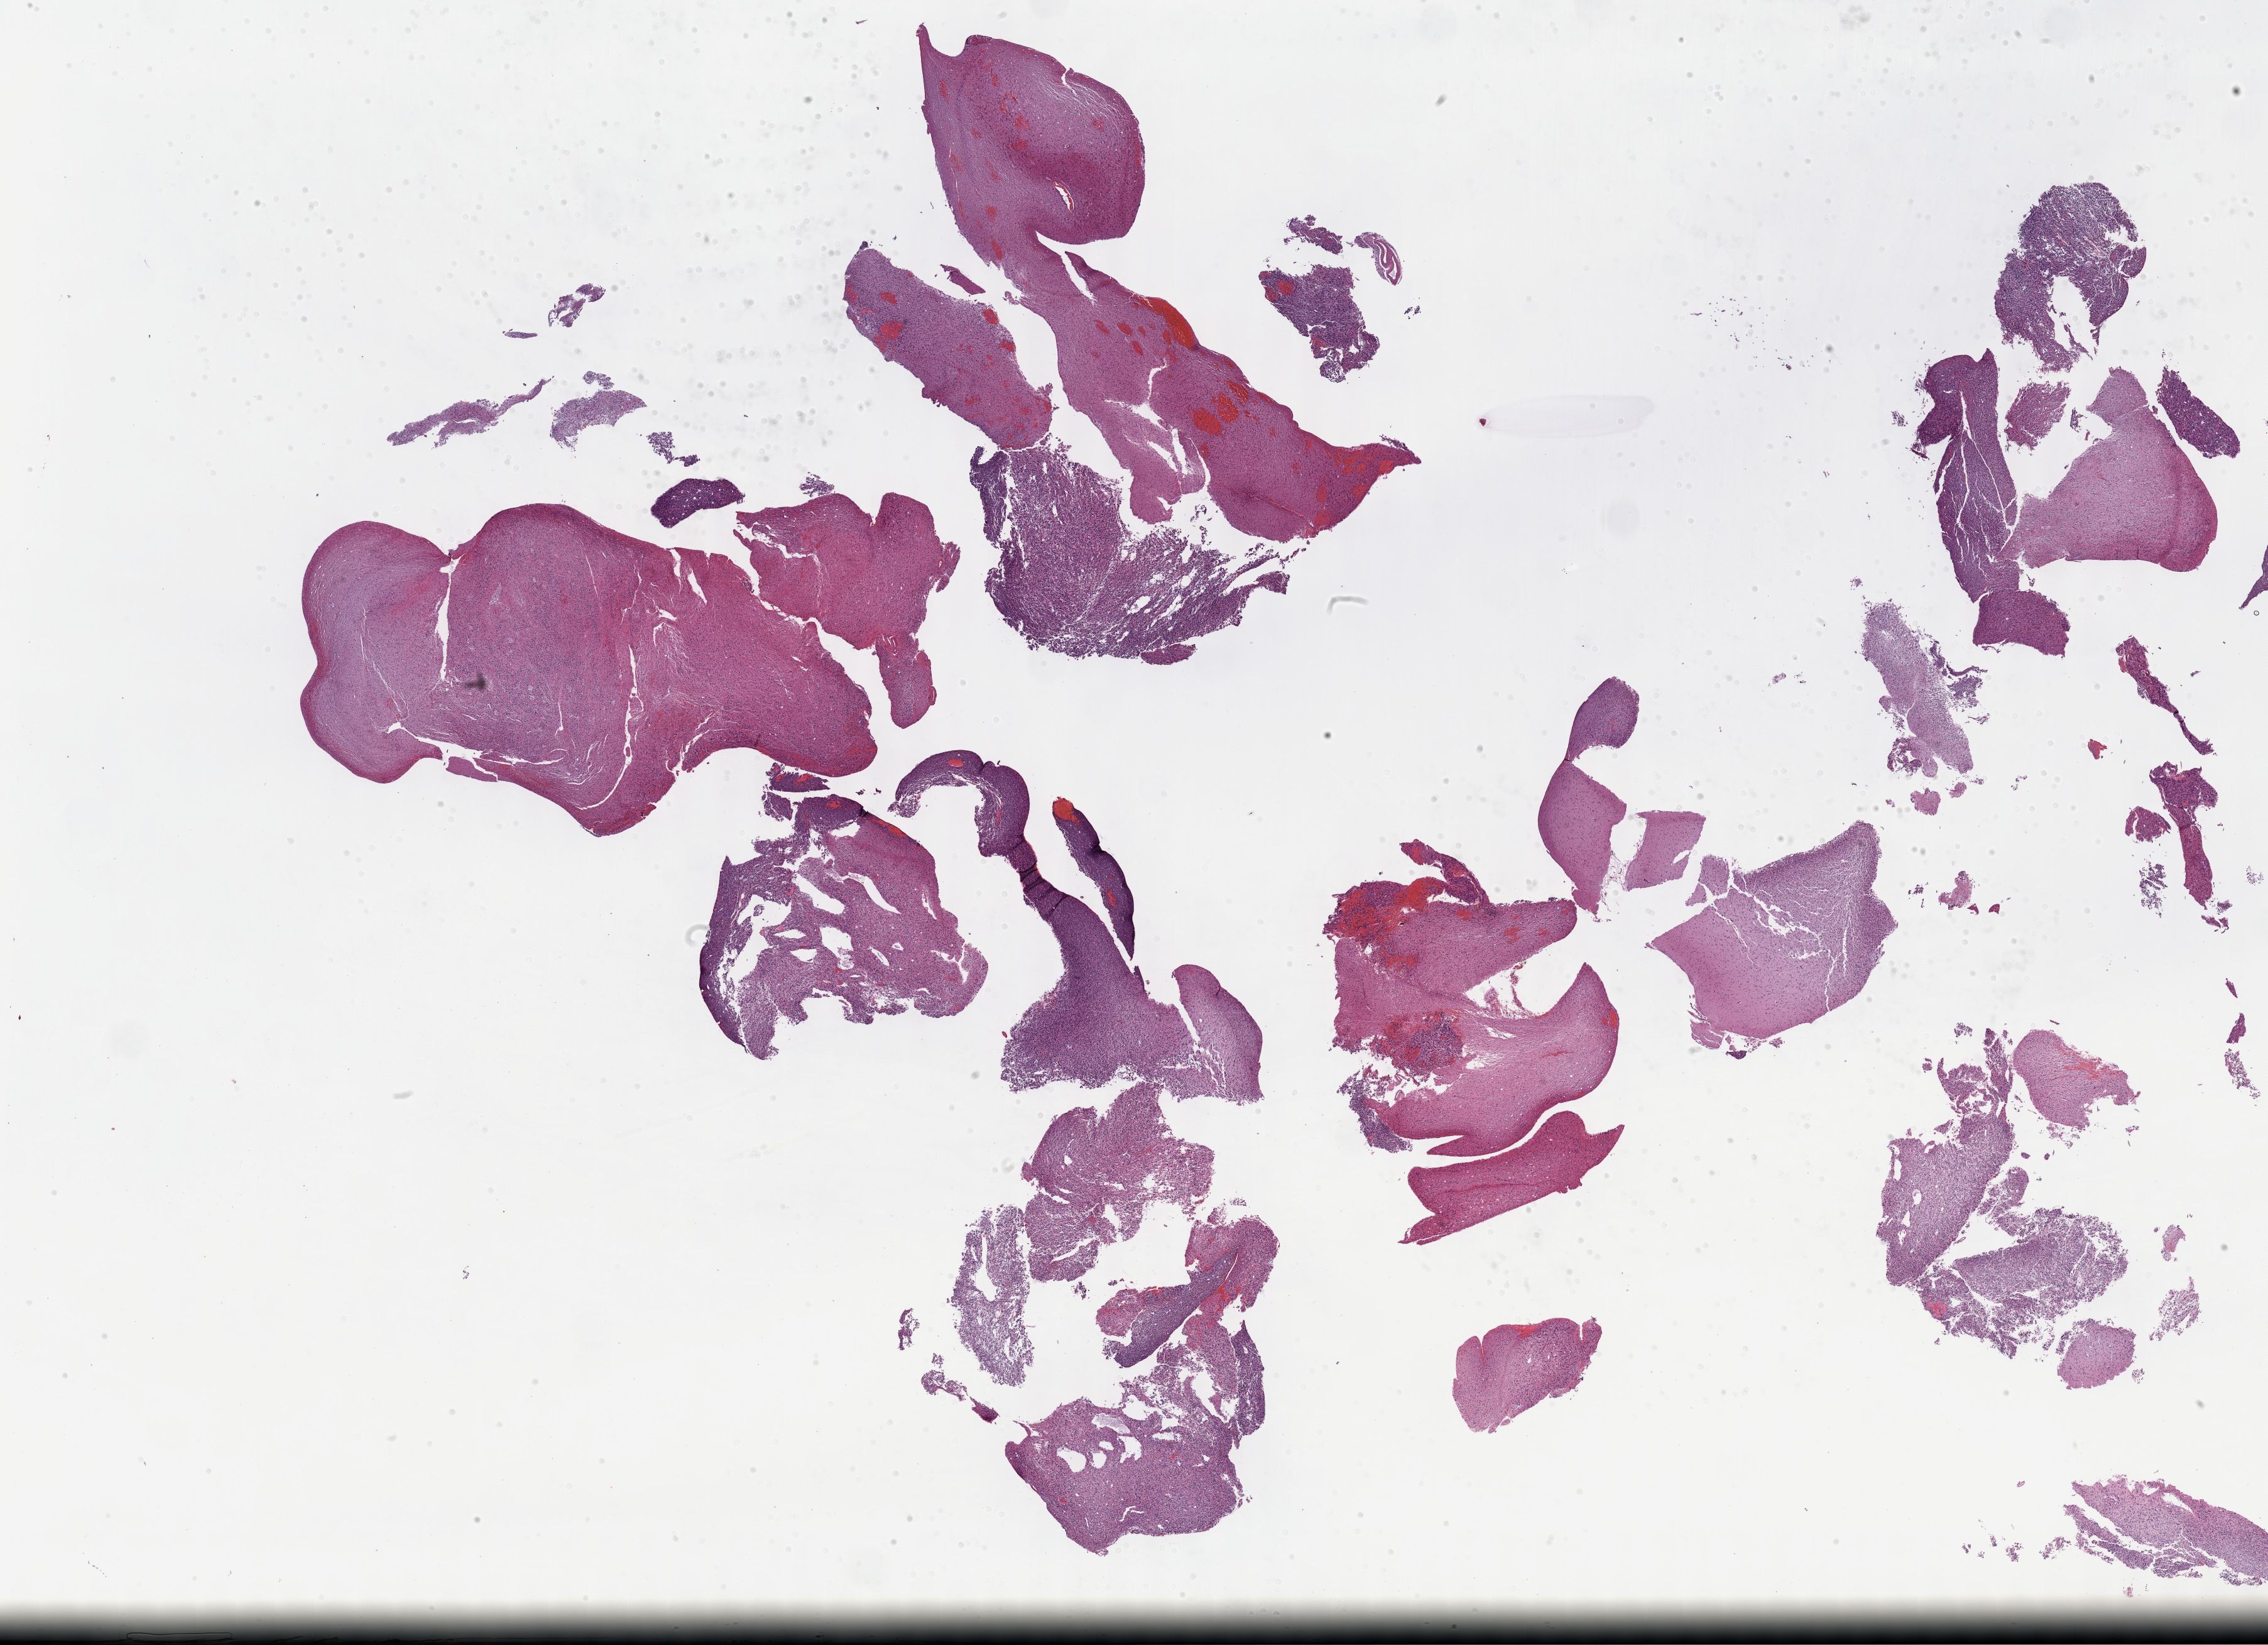
H&E whole-slide image, a low-resolution overview of the entire scanned area, about 29.2 x 21.2 mm (from a 40x scan), formalin-fixed paraffin-embedded (FFPE) diagnostic section, primary tumour sample from the brain. Female, age 44 years at initial diagnosis. Histologic grade: G3 (poorly differentiated).
Histologic diagnosis: Astrocytoma, anaplastic (cerebrum).